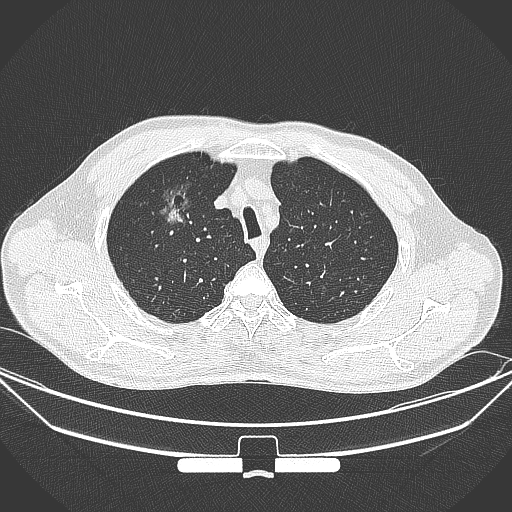
Chest CT, one axial slice; slice 283 of 355 in the series (ordered by position); 120 kVp; lung window (W 1500 / L -600 HU); 1 mm slice thickness; 512 × 512 image matrix, field of view 399 × 399 mm. Patient: male, 67 years. From the clinical record (not read from this slice): clinical TNM (as recorded): T1c N0 M0.
Annotated regions visible in this slice (rectangle marked by the reading radiologist):
- lung tumour (recorded histology: adenocarcinoma): box from (x=156, y=175) to (x=202, y=231) px